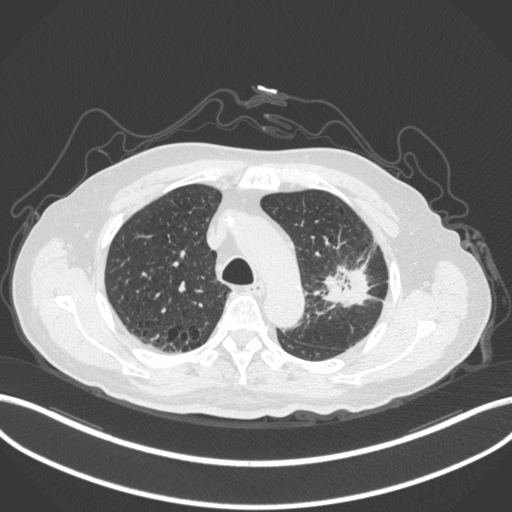
Chest CT, one axial slice; slice 218 of 331 in the series (ordered by position); reconstruction kernel B31f; lung window (W 1500 / L -600 HU); 1 mm slice thickness; 512 × 512 image matrix. Male patient, age 79 years. Case-level facts recorded for this patient, not image findings: clinical TNM (as recorded): T2a N1 M1.
Outlined on this slice (rectangle marked by the reading radiologist):
- lung tumour (recorded histology: adenocarcinoma): bounding box <315,257,374,311> (left, top, right, bottom; pixels)